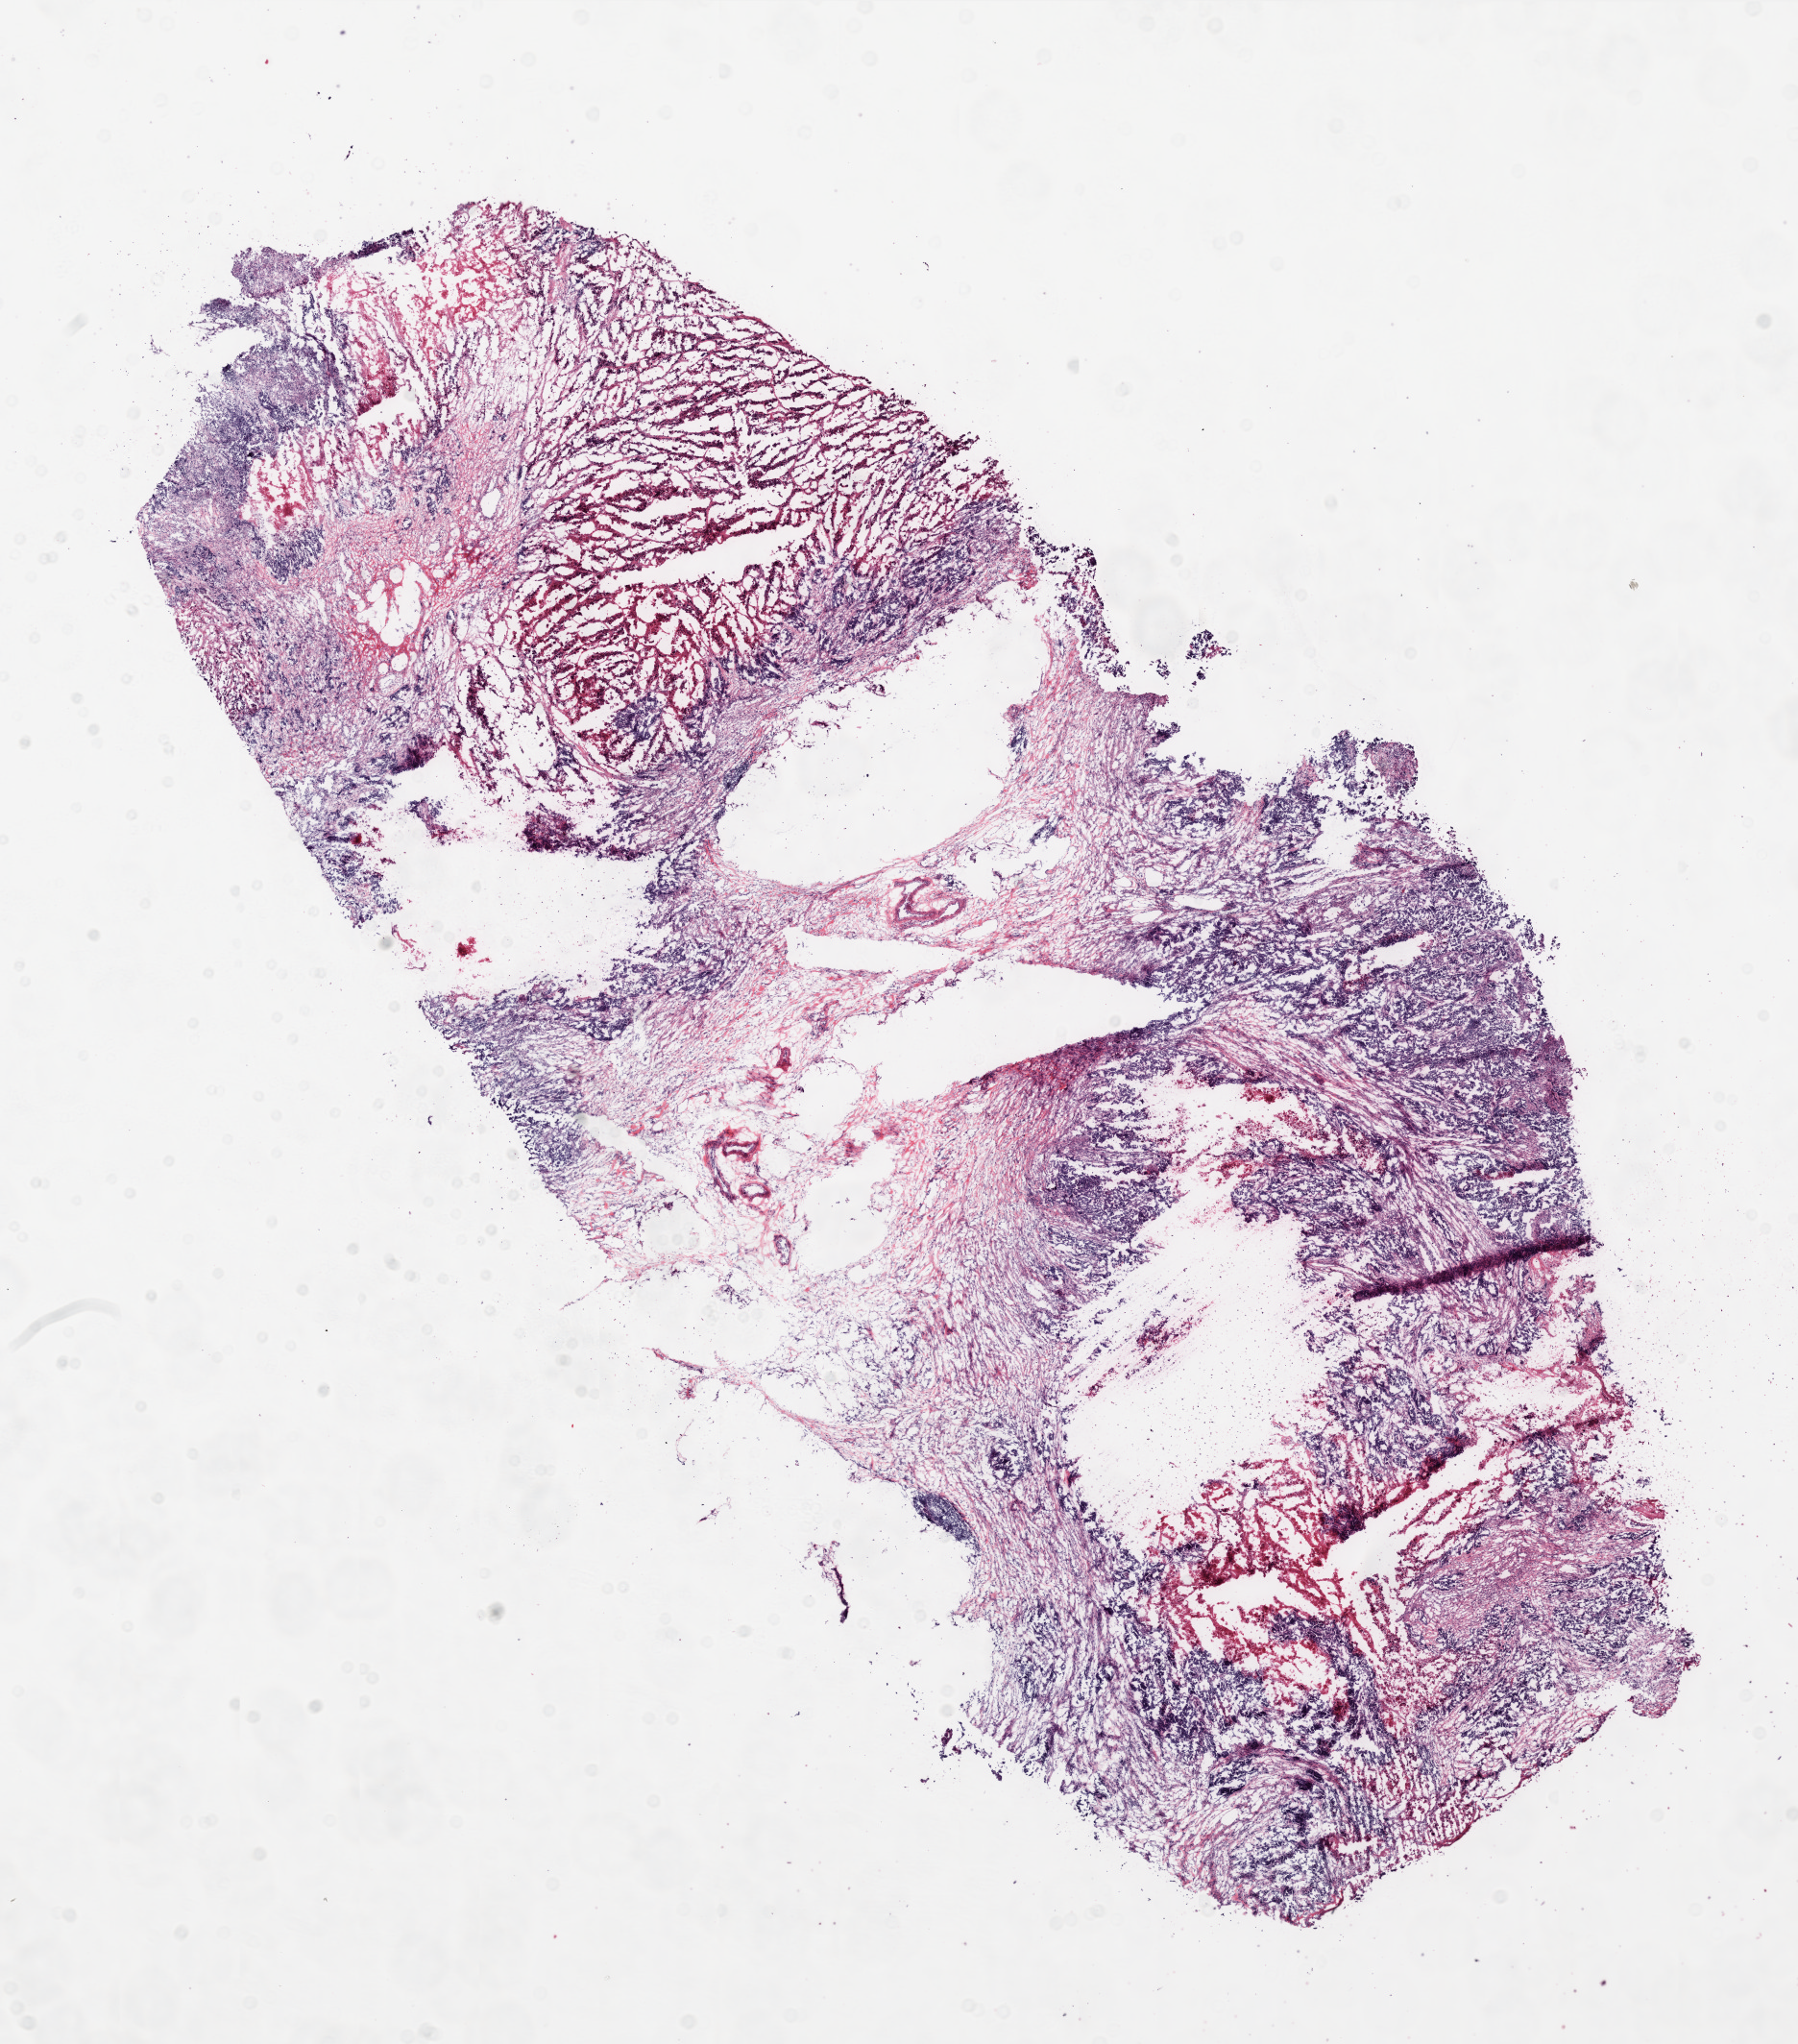
Digitized H&E tissue section (whole slide), whole scanned area (about 15.0 x 17.0 mm, acquisition: 20x scan) shown as a low-resolution overview. Frozen section. Sample: primary tumour, ovary. Female, age 54 years at initial diagnosis. Histologic grade: G3 (poorly differentiated). Composition of this section per pathologist review: tumour cells 65%, tumour nuclei 80%, normal cells 0%, stromal cells 20%, necrosis 15%. Inflammatory infiltration, as recorded: lymphocyte infiltration 100%.
• FIGO stage: IIIC
• pathologic diagnosis: Serous cystadenocarcinoma, NOS